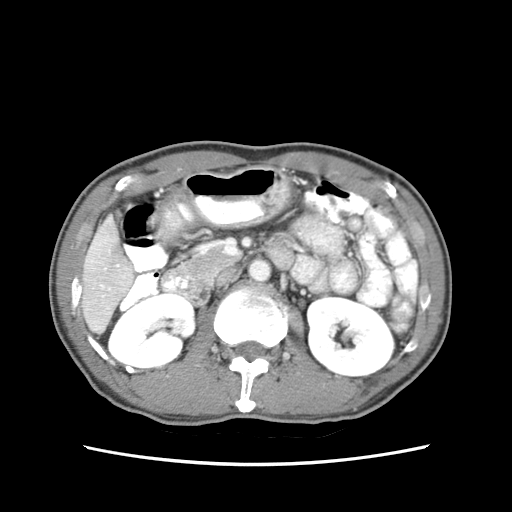
Contrast-enhanced abdominal CT (liver protocol), one axial slice; slice 20 of 79 in the series (ordered by position); reconstruction kernel STANDARD; soft-tissue window (W 400 / L 40 HU); 2.5 mm slice thickness; 512 × 512 image matrix. From the clinical record (not read from this slice): diagnosis: hepatocellular carcinoma (patient treated with transarterial chemoembolisation; whether this scan precedes or follows treatment is not stated here); TNM stage (as recorded): Stage-IIIB; Child-Pugh class: A; tumour differentiation: moderately differentiated; tumour nodularity: multinodular.
Outlined on this slice (semi-automatic segmentation, software-assisted and operator-edited):
- liver parenchyma outside the tumour (the mass and vessels are separate outlines, so this box may not span the whole liver): box from (x=82, y=216) to (x=134, y=332) px
- liver vessels: (x=86, y=231)–(x=132, y=308)